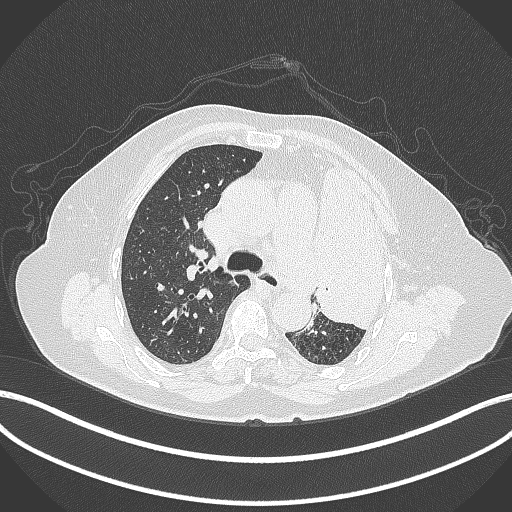
Chest CT, one axial slice; slice 259 of 399 in the series (ordered by position); reconstruction kernel B70f; lung window (W 1500 / L -600 HU); 512 × 512 image matrix, field of view 400 × 400 mm. Female patient, age 75 years. From the clinical record (not read from this slice): clinical TNM (as recorded): T3 N3 M1.
Annotated regions visible in this slice (bounding box drawn by a radiologist):
- lung tumour (recorded histology: adenocarcinoma): bounding box [x1, y1, x2, y2] px = [308, 155, 398, 331]